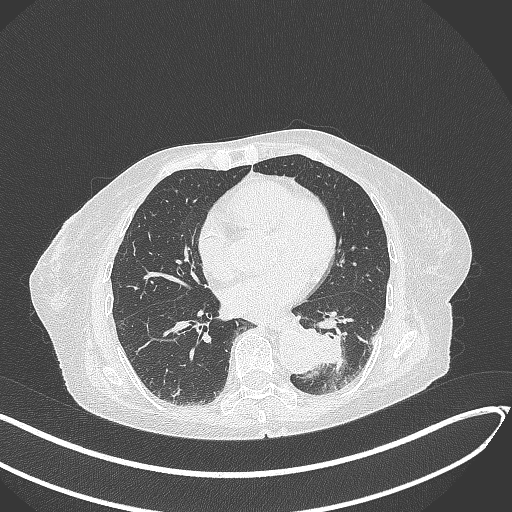
Chest CT, one axial slice. Slice 102 of 324 in the series (ordered by position). Lung window (W 1500 / L -600 HU). 1 mm slice thickness. 512 × 512 image matrix. Patient: female, 82 years. Case-level facts recorded for this patient, not image findings: clinical TNM (as recorded): T1b N0 M1.
Structures marked on this image (rectangle marked by the reading radiologist):
- lung tumour (recorded histology: adenocarcinoma): bounding box [x1, y1, x2, y2] px = [304, 321, 350, 374]